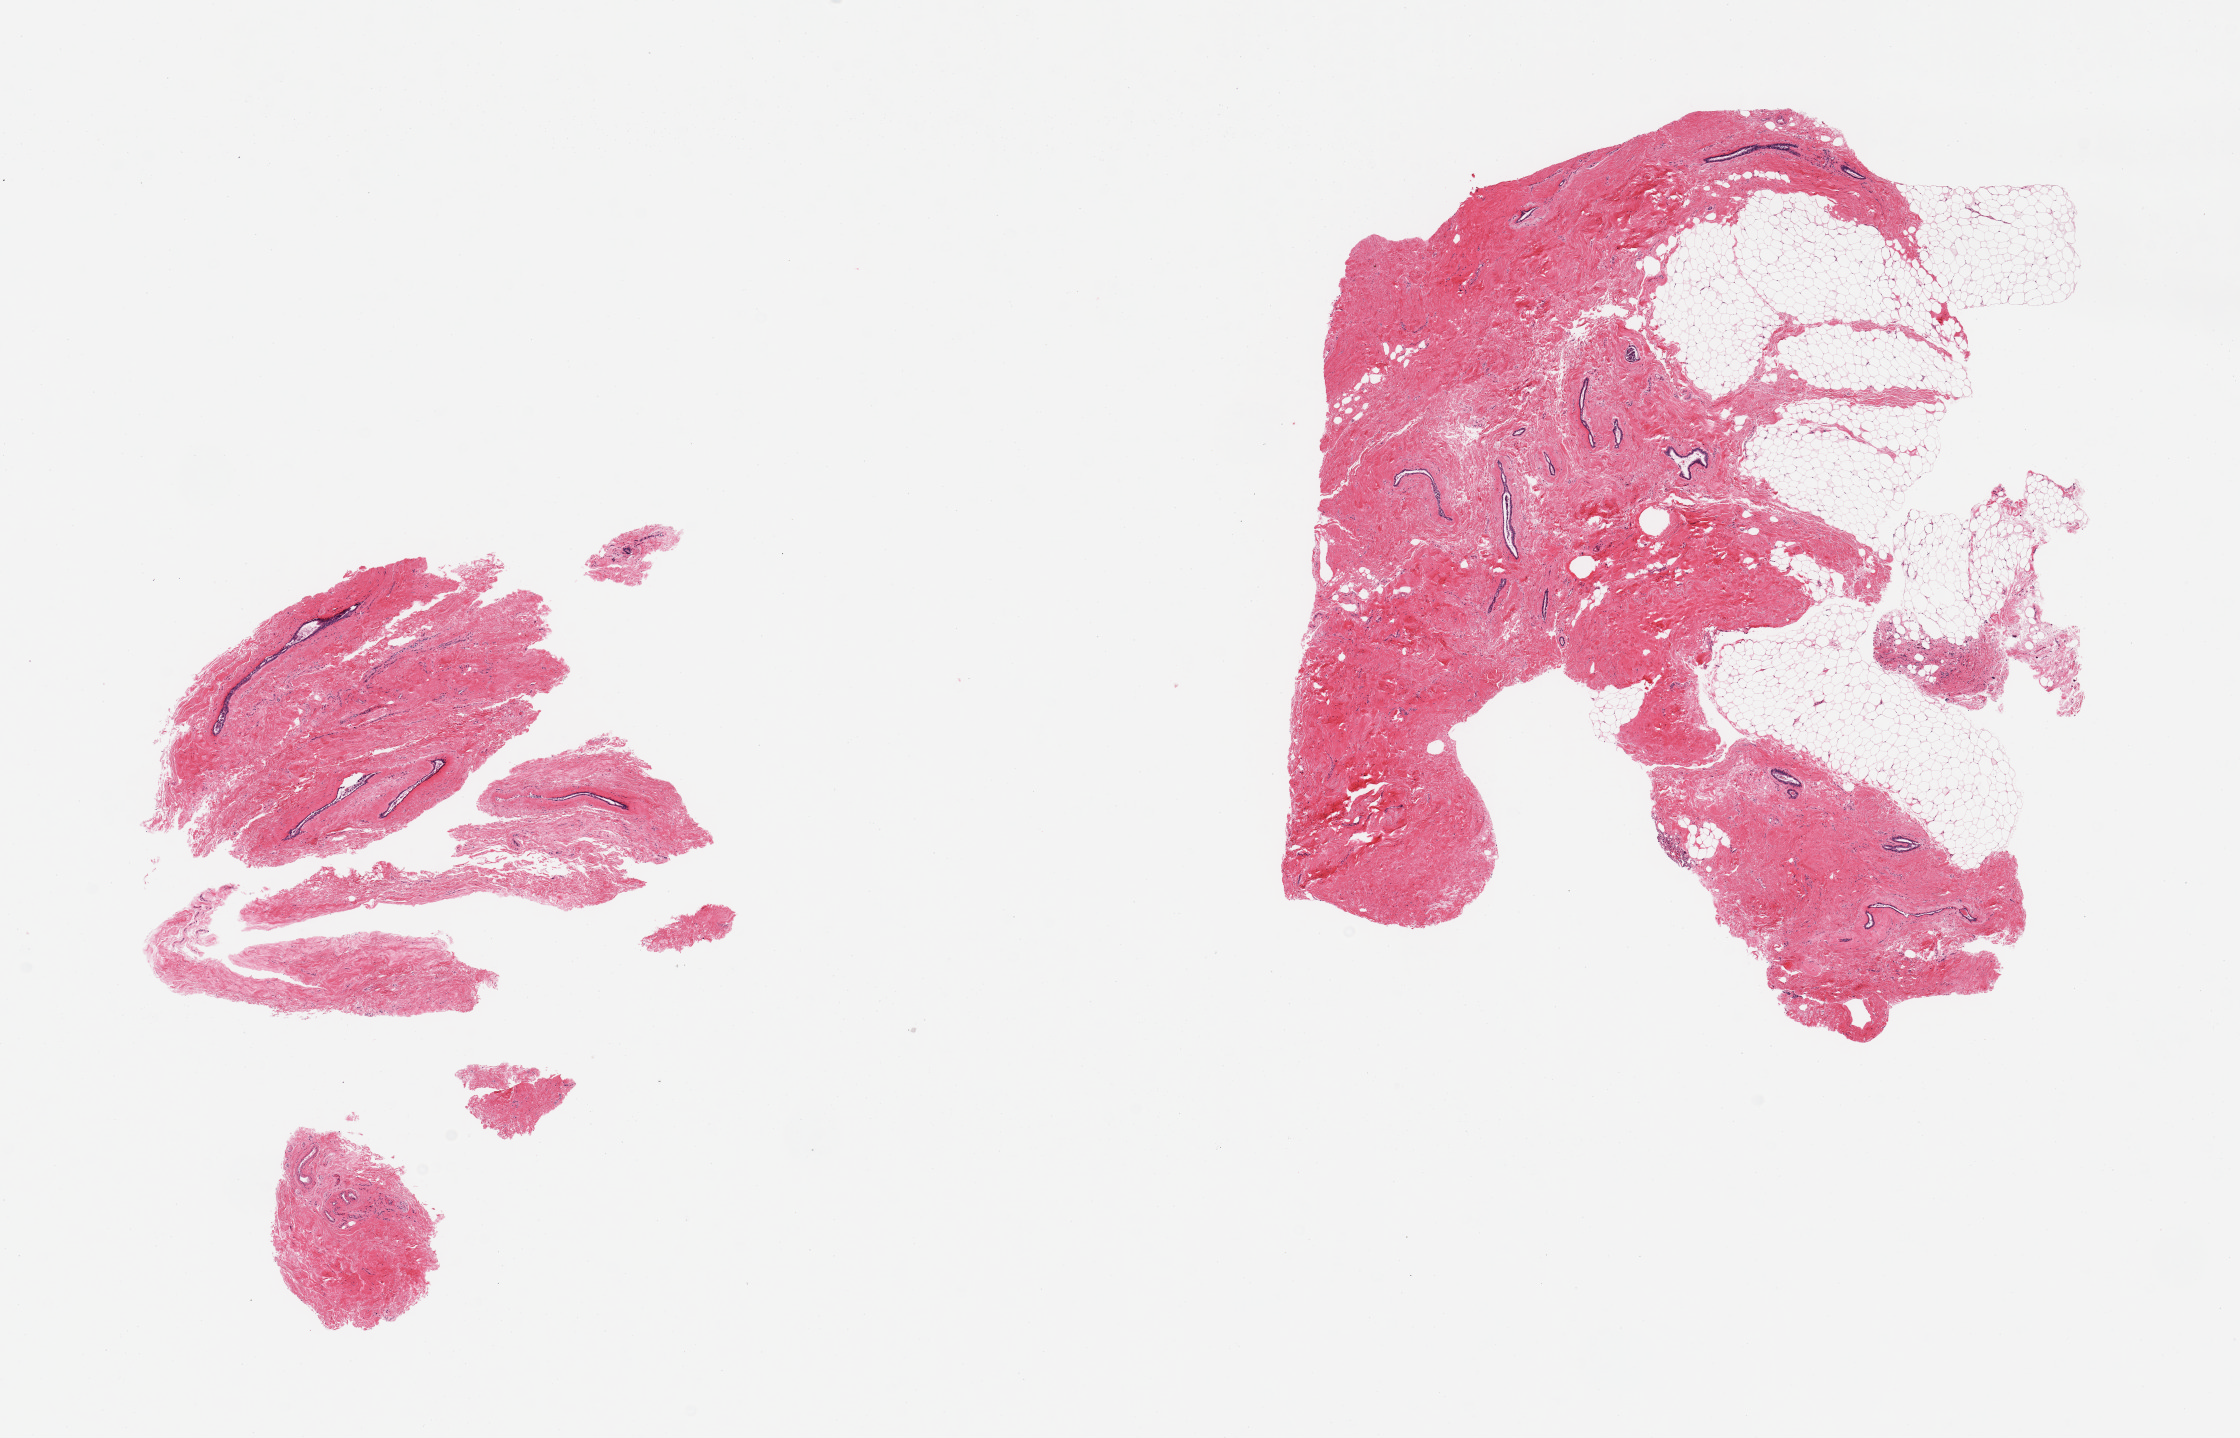
Whole-slide image, haematoxylin and eosin stain, brightfield, shown as a low-resolution overview of the whole scanned area (about 17.7 x 11.4 mm); PAXgene-fixed, paraffin-embedded tissue; target tissue: breast; donor tissue sample.
• reviewer comment on this tissue sample: 2 pieces; proliferating ducts and fibrous stroma consistent with gynecomastoid hyperplasia